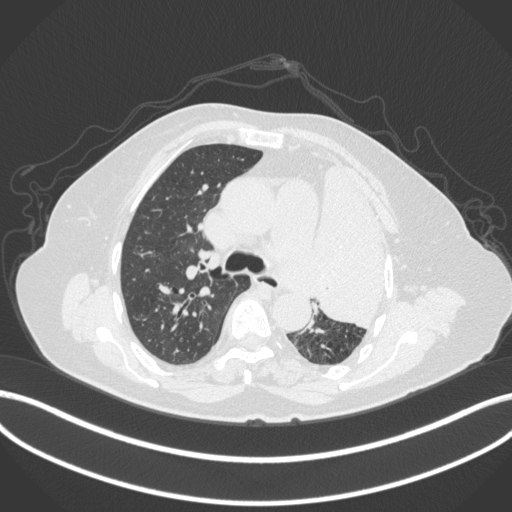
Chest CT, one axial slice. Slice 256 of 399 in the series (ordered by position). Reconstruction kernel B31f. 120 kVp. Lung window (W 1500 / L -600 HU). 1 mm slice thickness. 512 × 512 image matrix, field of view 400 × 400 mm. Patient: female, 75 years. From the clinical record (not read from this slice): clinical TNM (as recorded): T3 N3 M1.
Structures marked on this image (rectangle marked by the reading radiologist):
- lung tumour (recorded histology: adenocarcinoma): bounding box [x1, y1, x2, y2] px = [312, 160, 394, 332]